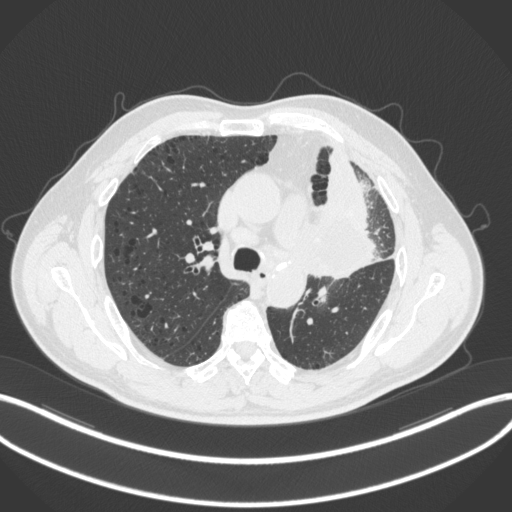
Chest CT, one axial slice. 120 kVp. Lung window (W 1500 / L -600 HU). 1 mm slice thickness. 512 × 512 image matrix, field of view 400 × 400 mm. Patient: male, 68 years. From the clinical record (not read from this slice): clinical TNM (as recorded): T3 N3 M1.
Structures marked on this image (bounding box drawn by a radiologist):
- lung tumour (recorded histology: adenocarcinoma): bounding box <302,200,382,286> (left, top, right, bottom; pixels)